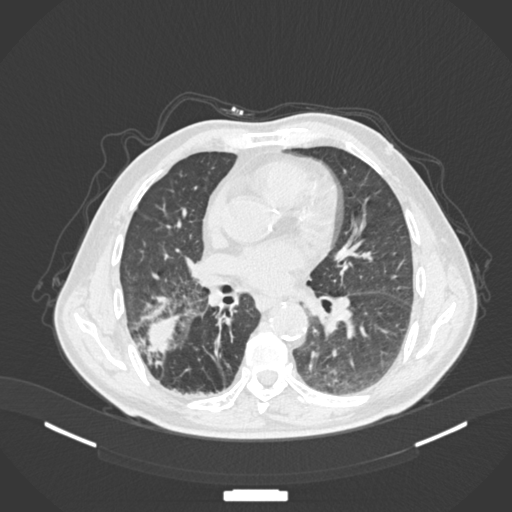
Chest CT, one axial slice. Position 77 of 201 along the scan axis. Reconstruction kernel B30f. Lung window (W 1500 / L -600 HU). 512 × 512 image matrix. Male patient, age 72 years. Case-level facts recorded for this patient, not image findings: clinical TNM (as recorded): T3 N2 M0.
Structures marked on this image (bounding box drawn by a radiologist):
- lung tumour (recorded histology: adenocarcinoma): bounding box <139,307,184,359> (left, top, right, bottom; pixels)